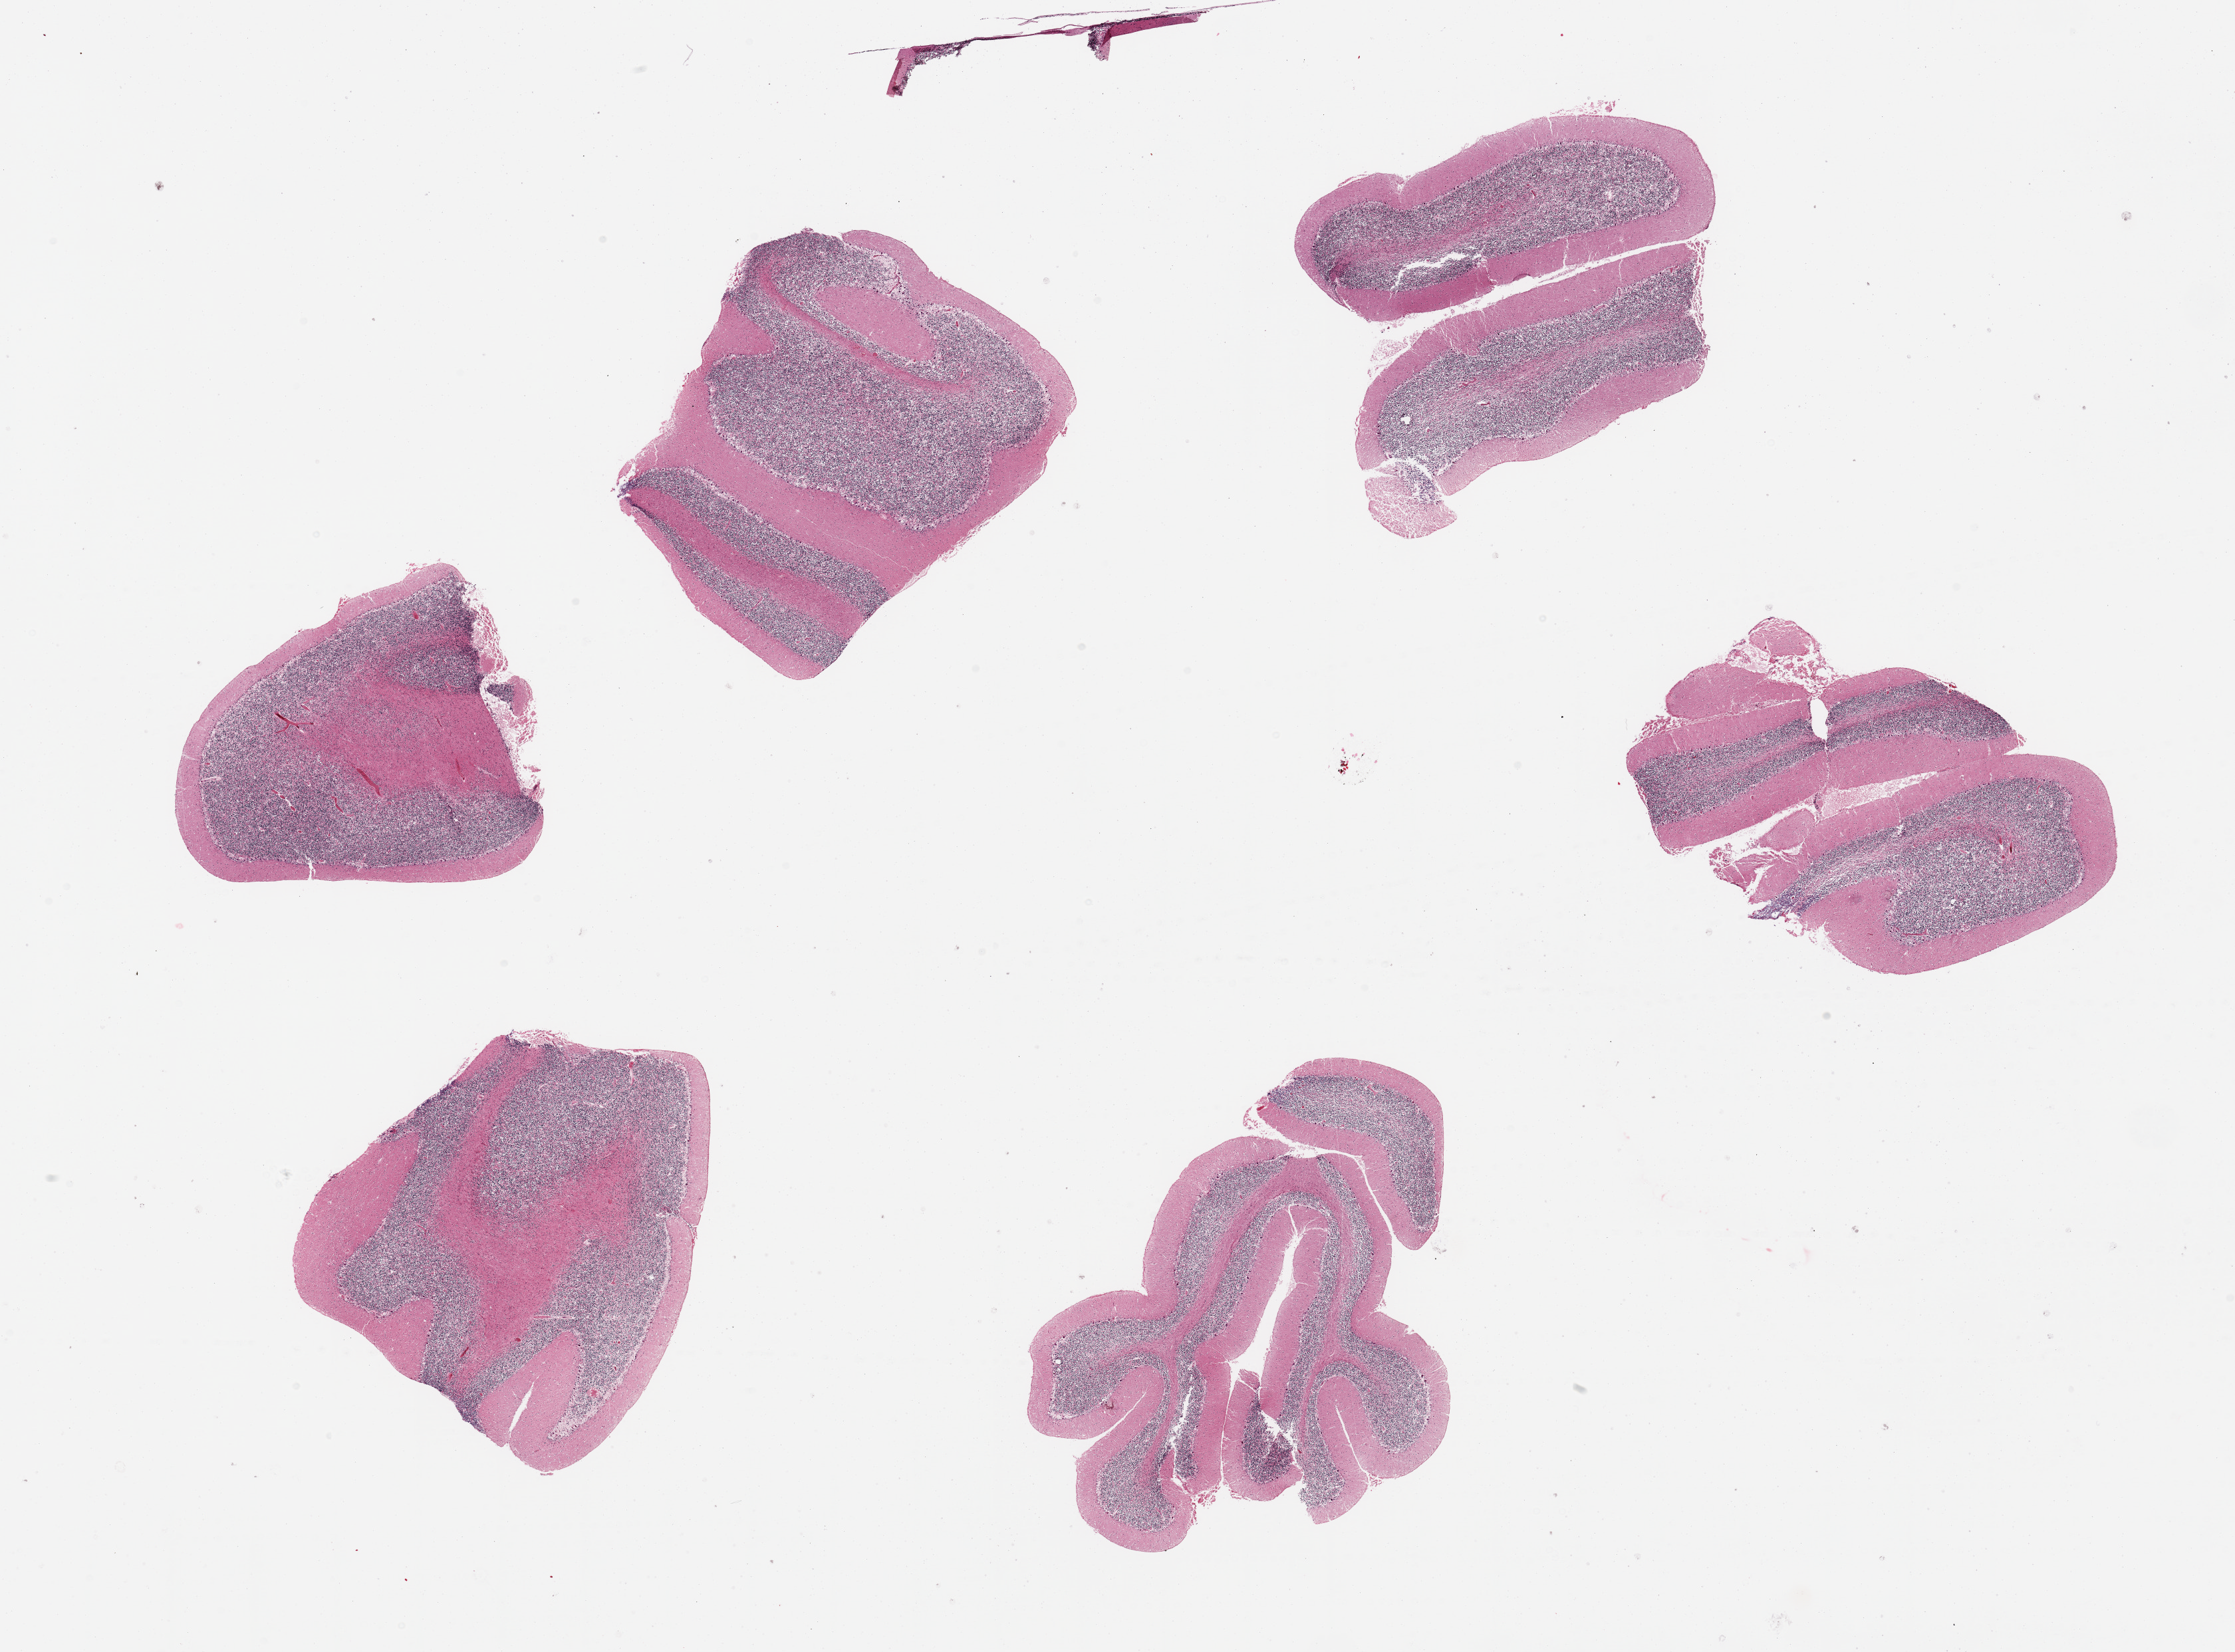
Haematoxylin and eosin whole-slide image, brightfield — shown as a low-resolution overview of the whole scanned area (about 26.6 x 19.7 mm, slide scanned at 20x); PAXgene-fixed, paraffin-embedded tissue; target tissue: cerebellum; donor tissue sample. Donor sex: female.
Reviewer comment on this tissue sample: 6 pieces.